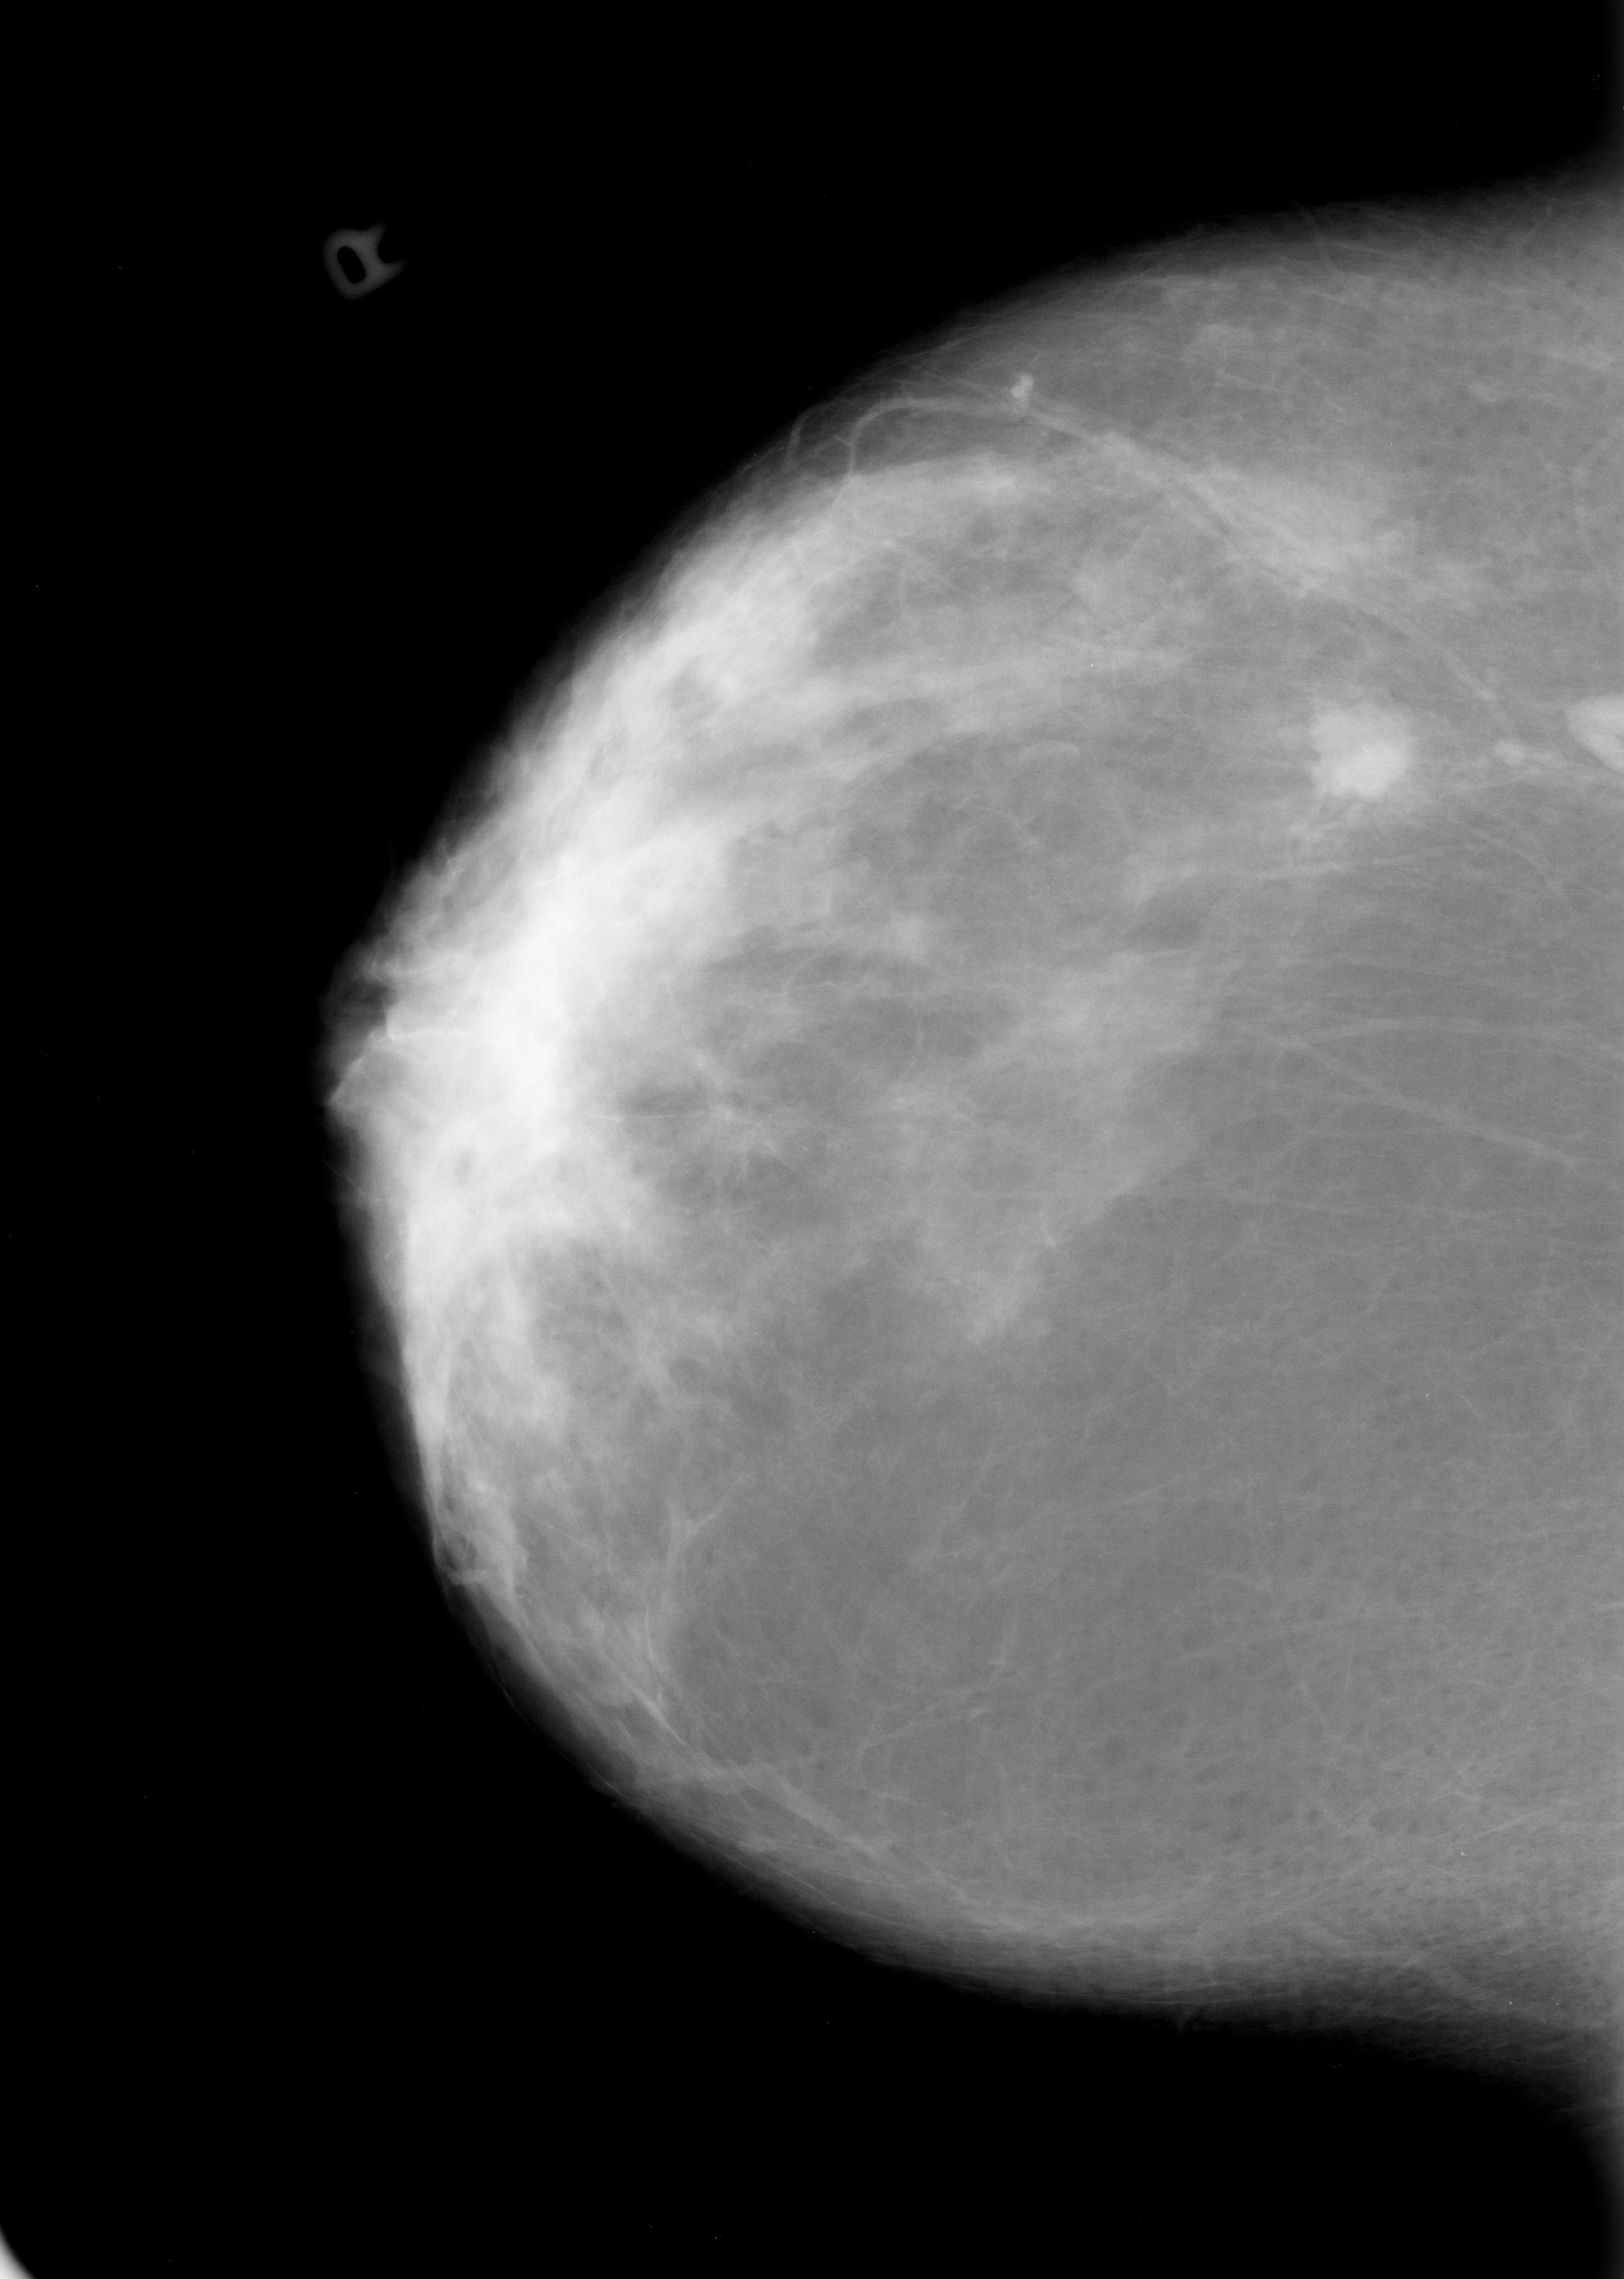
Scanned film-screen mammogram, right breast, CC view, BI-RADS breast density category 2 (scale 1–4).
Radiologist-marked abnormalities on this image: mass, shape lobulated, margins circumscribed / ill defined; BI-RADS assessment category 4; pathology result (as recorded, not read from the image): malignant.